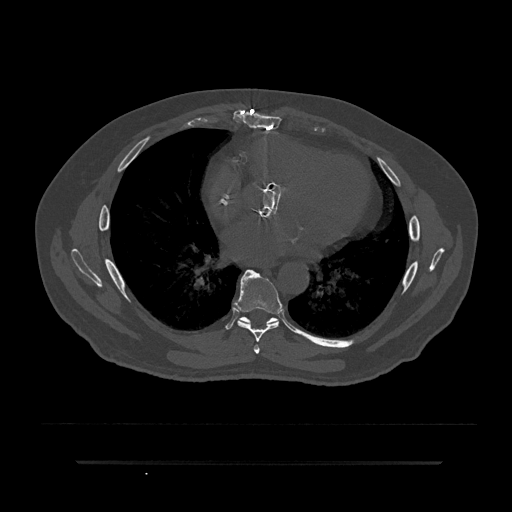
CT including the spine, one axial slice. Position 464 of 797 along the scan axis. 120 kVp. Bone window (W 1800 / L 400 HU). 0.5 mm slice thickness. 512 × 512 image matrix, field of view 464 × 464 mm. Male patient, age 59 years. From the clinical record (not read from this slice): primary cancer: bile ducts.
Structures marked on this image (semi-automatically segmented with operator editing):
- T6 vertebra: box from (x=254, y=345) to (x=260, y=354) px
- T7 vertebra: (x=233, y=269)–(x=282, y=342)
- T8 vertebra: (x=237, y=309)–(x=296, y=333)